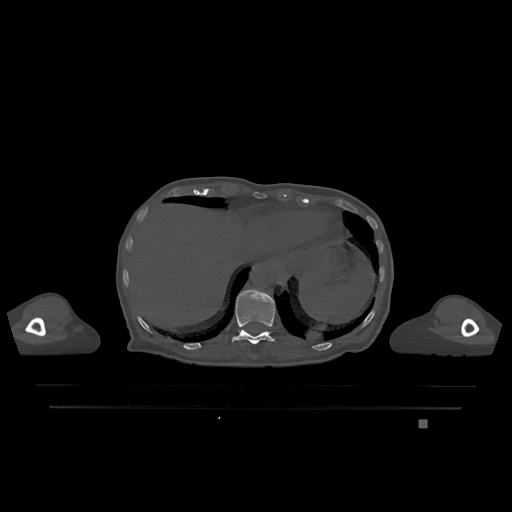
CT including the spine, one axial slice; slice 587 of 1317 in the series (ordered by position); bone window (W 1800 / L 400 HU); 0.5 mm slice thickness; 512 × 512 image matrix, field of view 500 × 500 mm. Patient: female, 74 years. Case-level facts recorded for this patient, not image findings: primary cancer: lung.
Outlined on this slice (semi-automatically segmented with operator editing):
- T11 vertebra: bounding box [x1, y1, x2, y2] px = [231, 289, 277, 344]